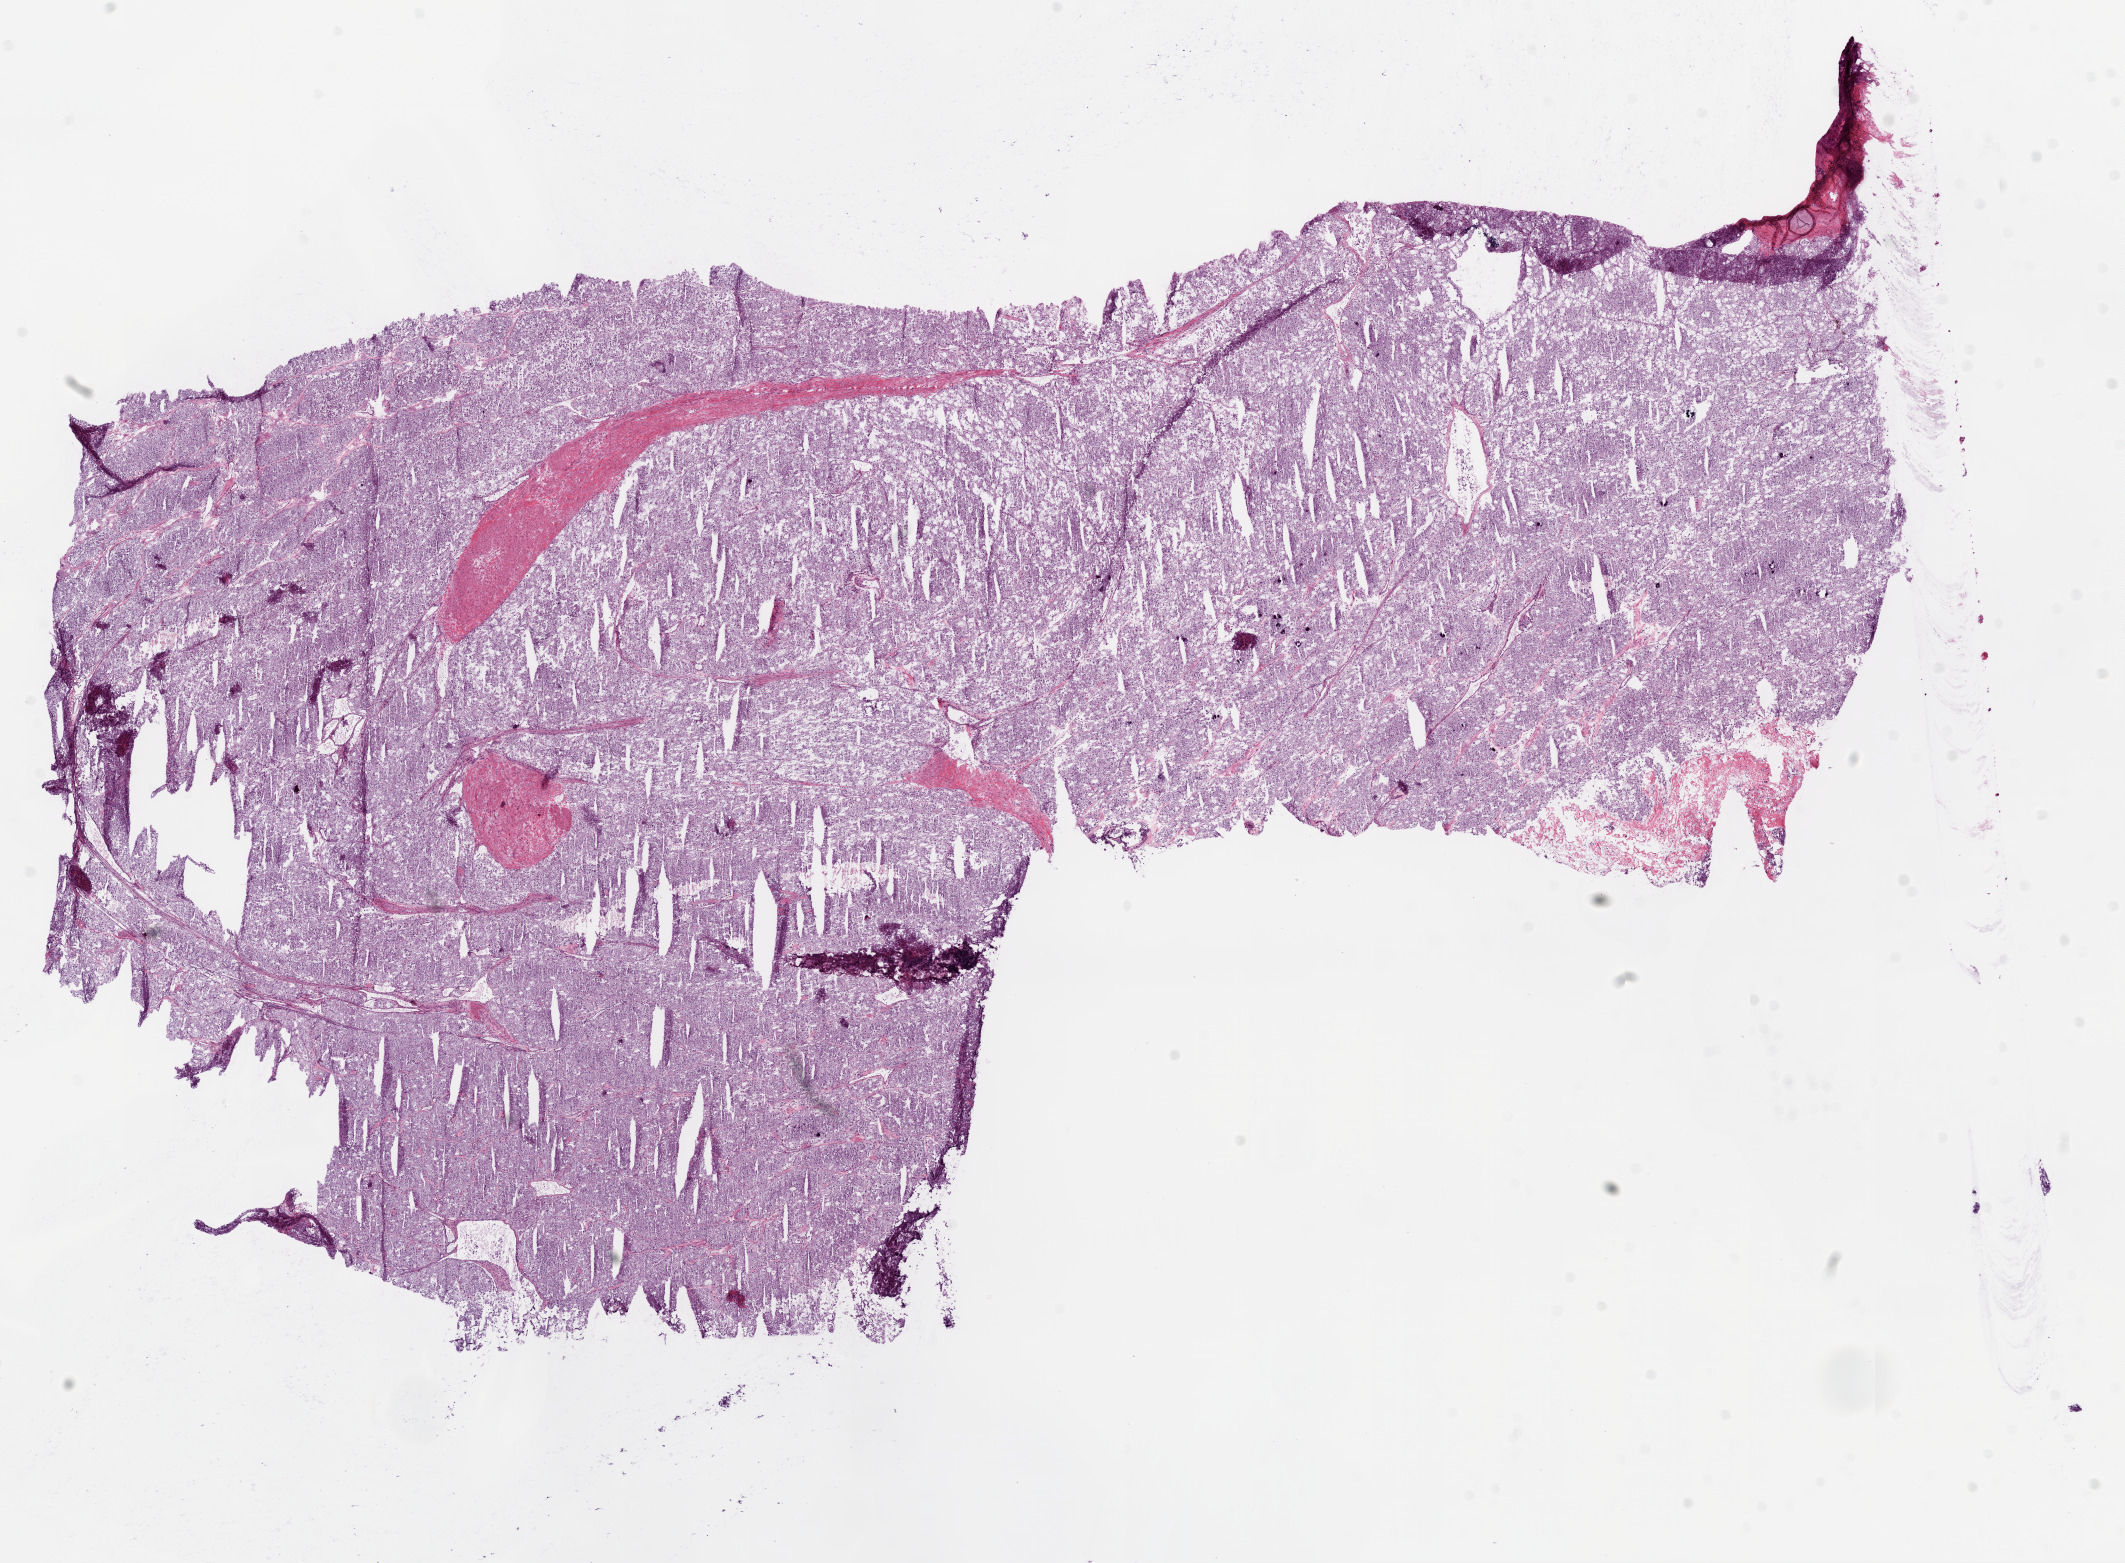
Digitized Hematoxylin and eosin (H&E) stained tissue section (whole slide), low-resolution overview of the scanned area, about 17.1 x 12.5 mm (from a 20x scan); frozen section from the bottom of the tissue portion; sample: primary tumour, kidney. Patient: male, age at initial diagnosis 59 years. Histologic grade: G2 (moderately differentiated). Slide review estimates, as recorded: tumour cells 93%, tumour nuclei 90%, normal cells 0%, stromal cells 5%, necrosis 2%.
Pathologic diagnosis: Clear cell adenocarcinoma, NOS. AJCC pathologic stage: II.